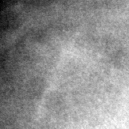
Cropped region of a digitized screen-film mammogram centred on a radiologist-marked abnormality, right breast, CC view, BI-RADS breast density category 3 (scale 1–4).
Marked abnormality: calcifications, morphology lucent center; BI-RADS assessment category 2; subtlety rating 3 on a 1 (subtle) to 5 (obvious) scale; benign without callback (not worked up further).